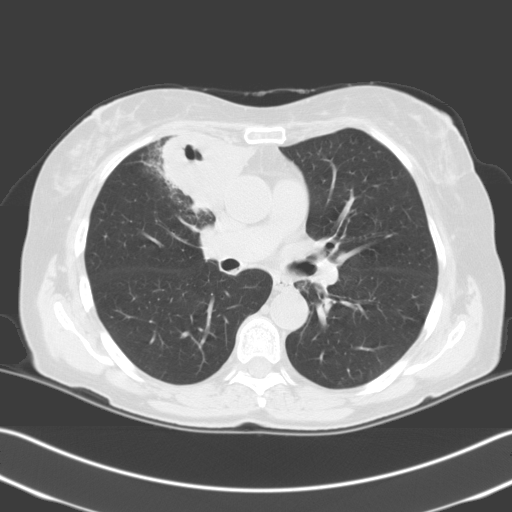
Low-dose screening chest CT, one axial slice. Lung window (W 1500 / L -600 HU). 3.2 mm slice thickness. 512 × 512 image matrix, field of view 348 × 348 mm.
Annotated regions visible in this slice (manually delineated by an expert):
- lesion 1 (tumor, upper lobe of right lung): bounding box (x1, y1, x2, y2) in pixels: (159, 132, 256, 212)